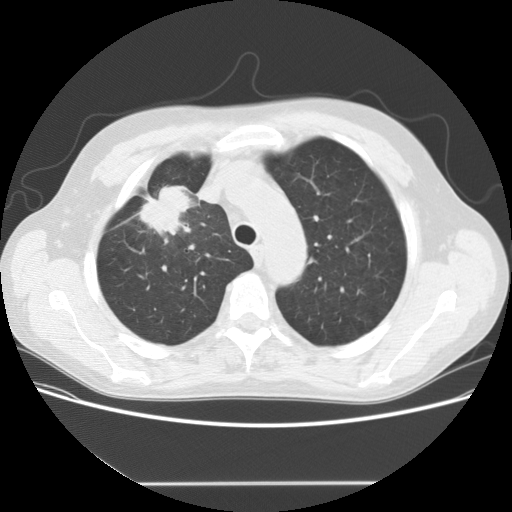
Low-dose screening chest CT, one axial slice; 120 kVp; lung window (W 1500 / L -600 HU); 2.5 mm slice thickness; 512 × 512 image matrix.
Outlined on this slice (manually delineated by an expert):
- lesion 1 (tumor, upper lobe of right lung): bounding box (x1, y1, x2, y2) in pixels: (139, 186, 193, 244)